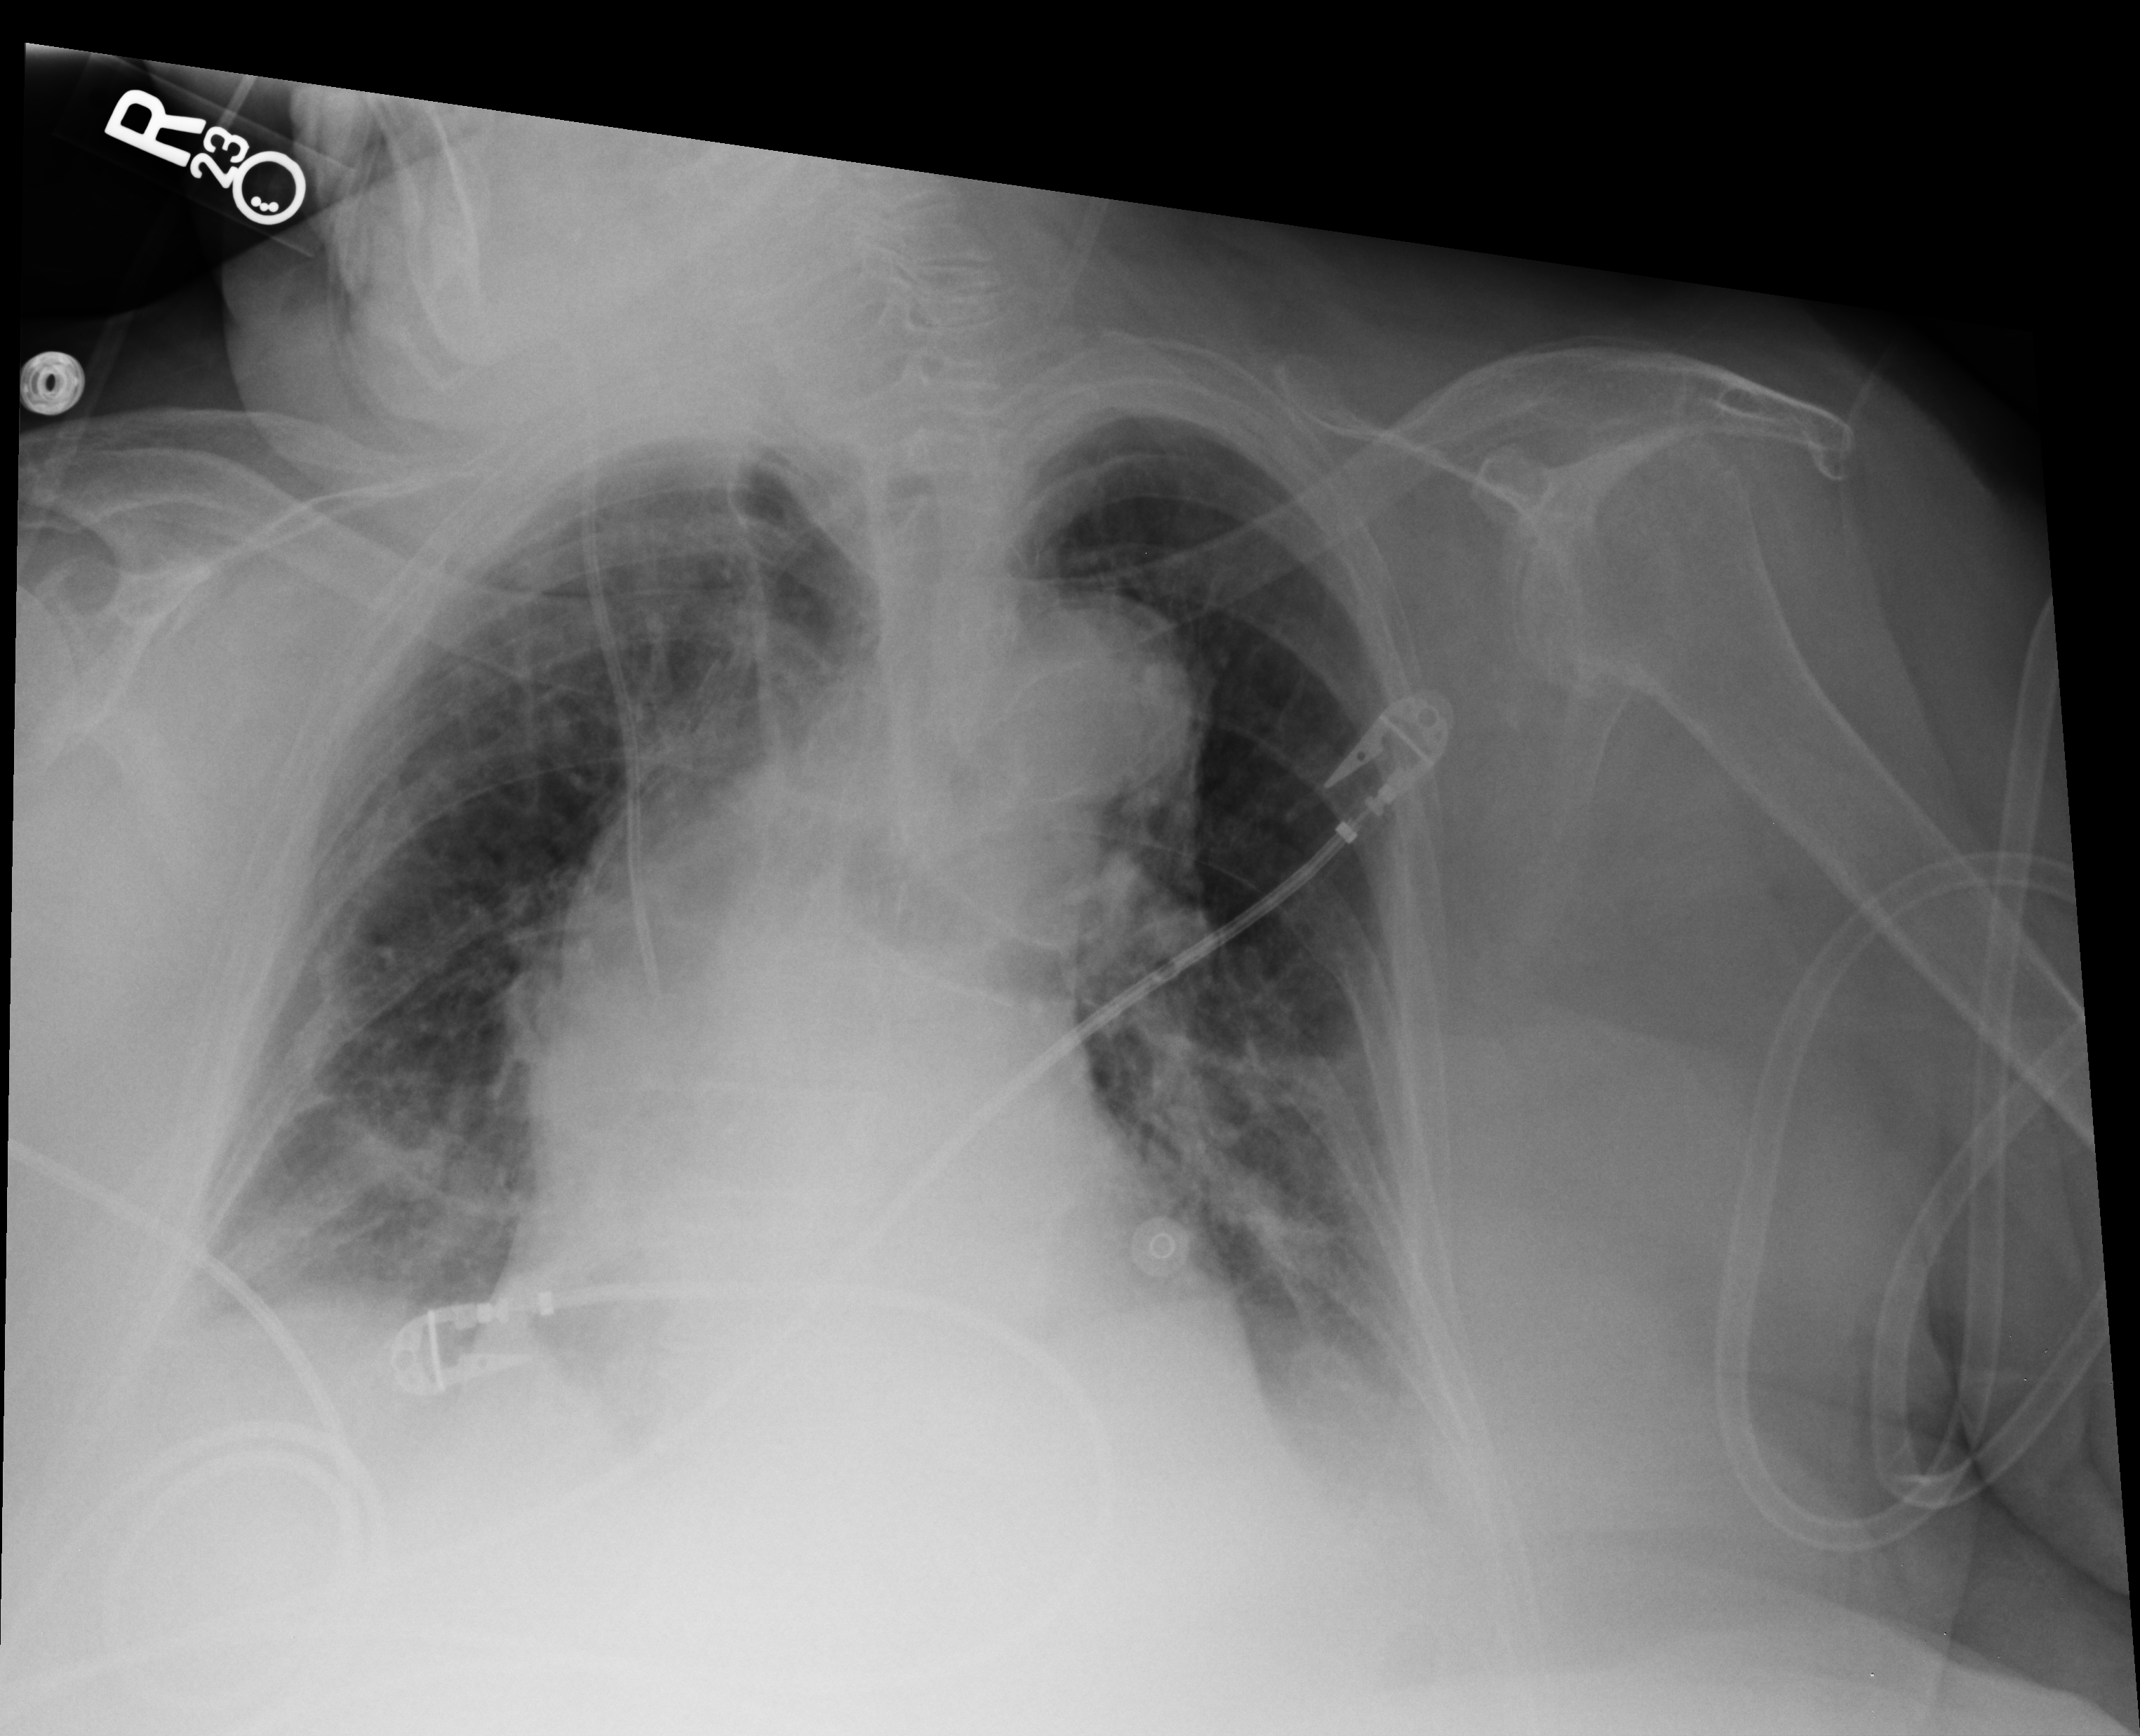
Portable chest radiograph; anteroposterior (AP) projection. Patient hospitalised with COVID-19; female, aged 75–90 years.
Hospital-stay facts (about this admission, not read from this image; timing relative to this image not recorded): mechanically ventilated during this hospital stay: no.